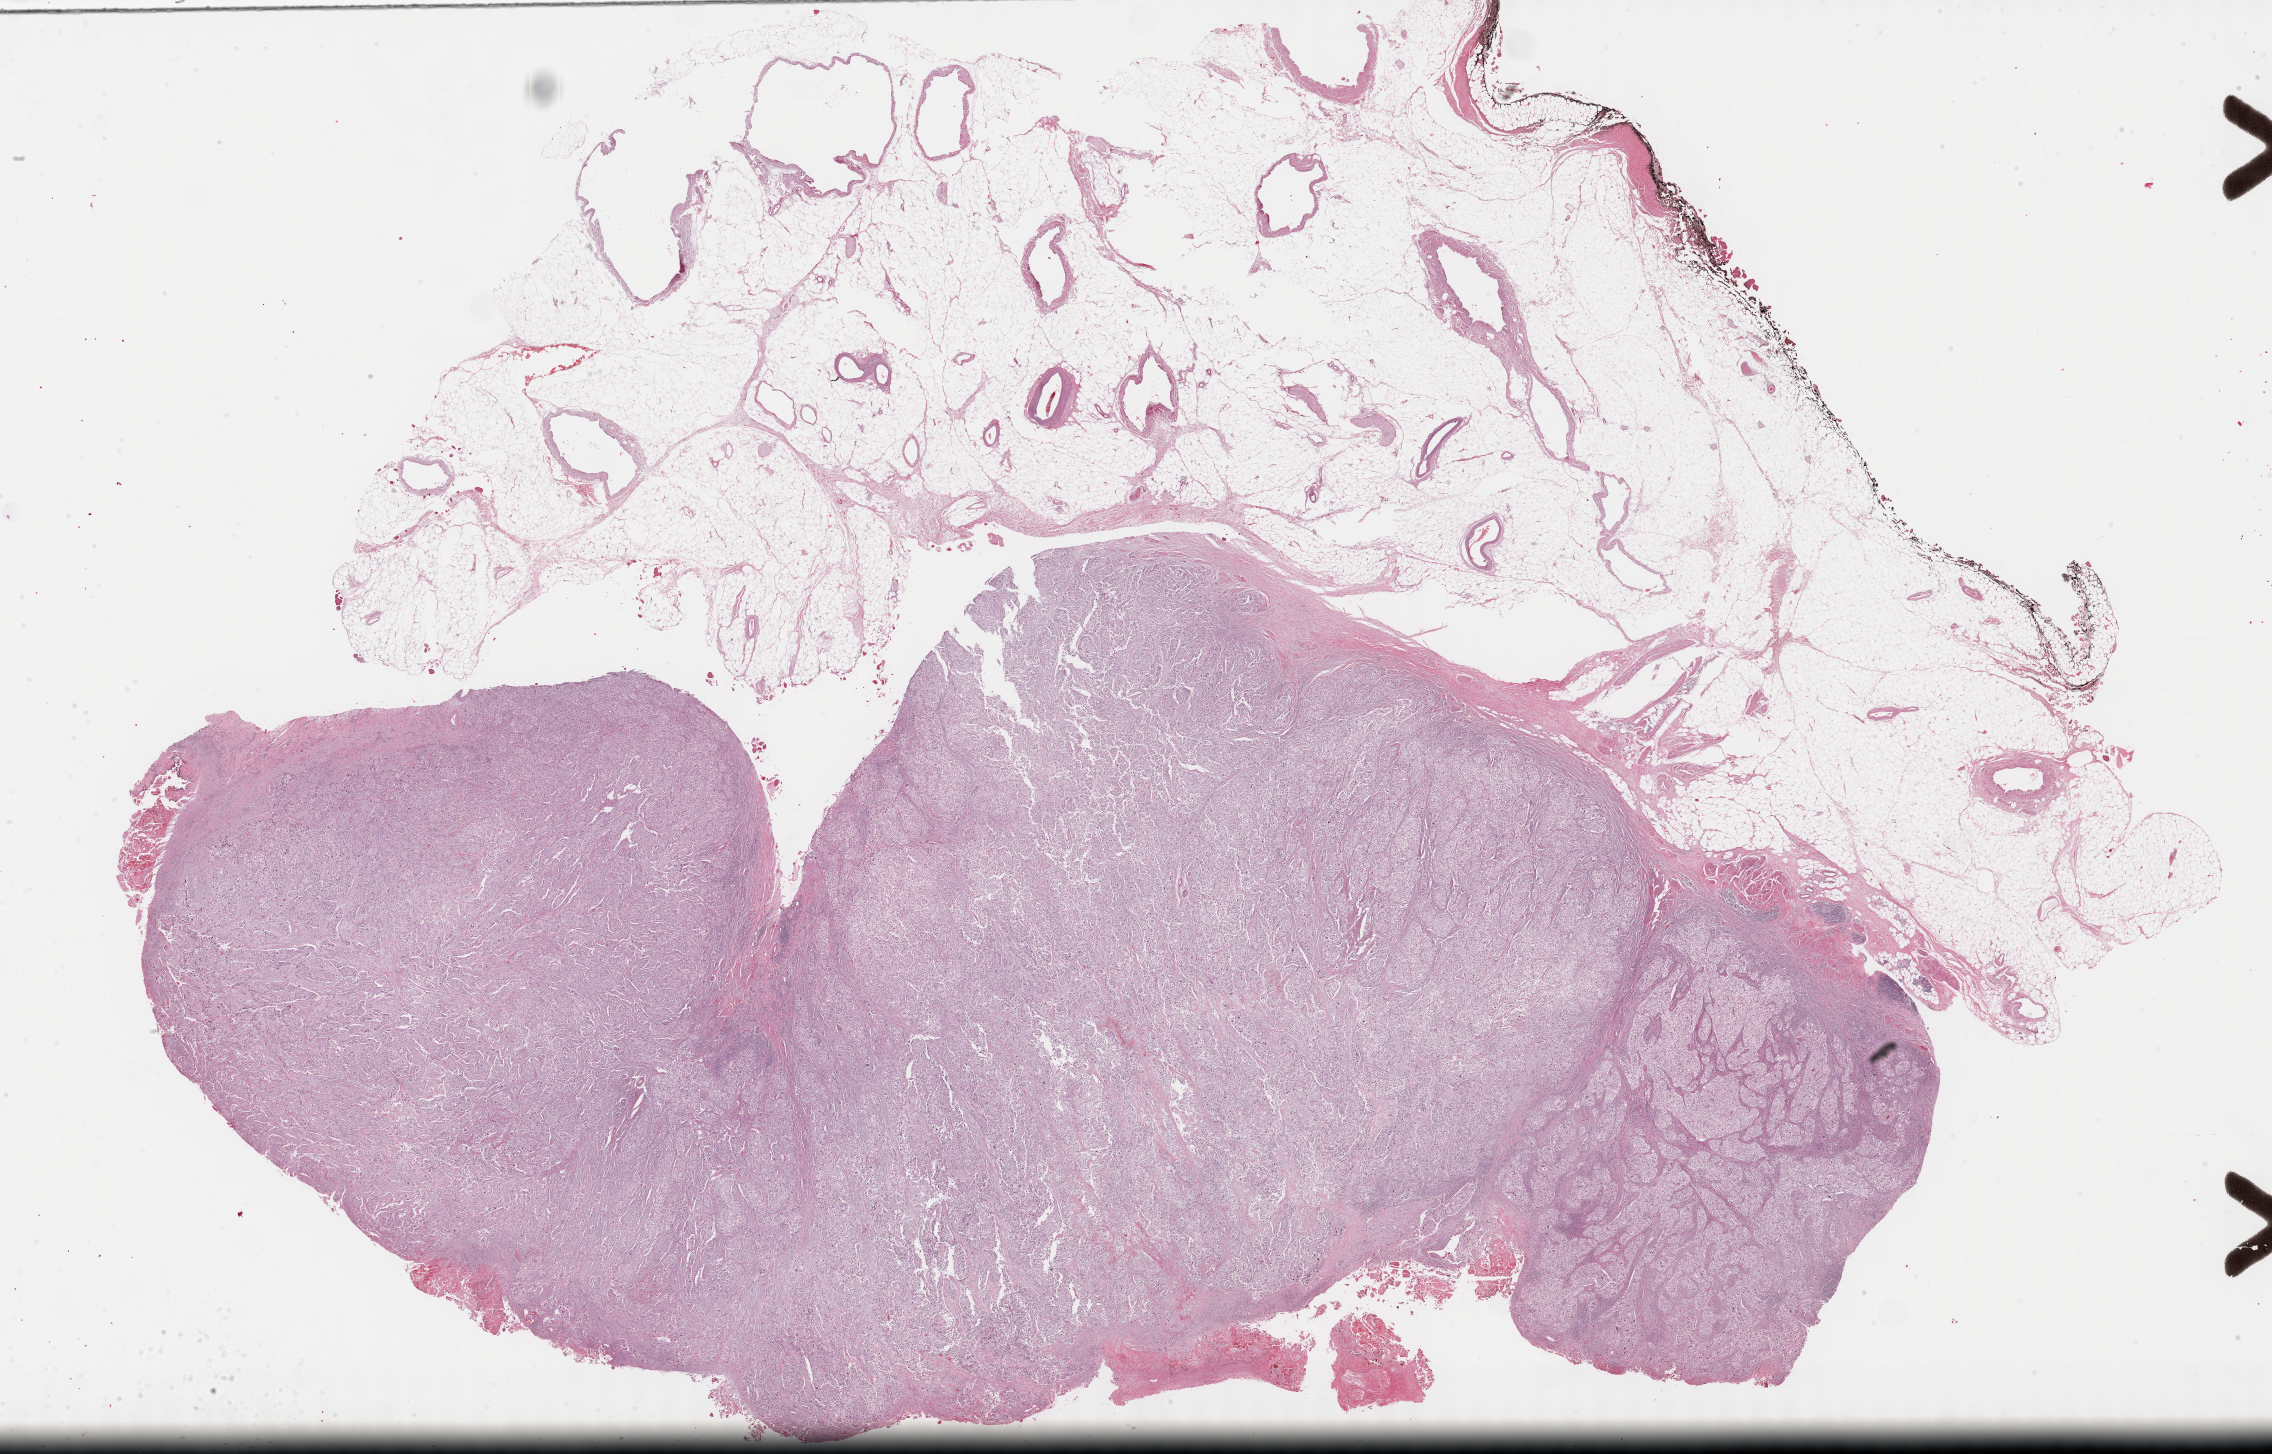
Digitized H&E-stained tissue section (whole slide) — a low-resolution overview of the entire scanned area, about 36.7 x 23.5 mm (acquisition: 40x scan), formalin-fixed paraffin-embedded (FFPE) diagnostic section, primary tumour sample from the bladder. Male patient; age at initial diagnosis 80 years.
Histologic diagnosis: Transitional cell carcinoma.